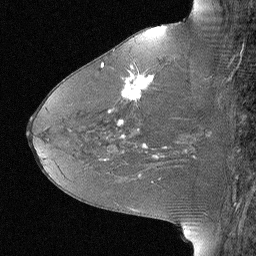
Breast MRI (dynamic contrast-enhanced), one sagittal slice. Position 31 of 64 along the scan axis. Dynamic contrast-enhanced study with each time point stored as its own series, time point 2 of 3 at this slice position (early post-contrast, ordered by acquisition time). 1.5 T. TE 4 ms, TR 30 ms. 256 × 256 image matrix. Female patient, age 46 years. From the clinical record (not read from this slice): setting: breast cancer imaged before/during neoadjuvant chemotherapy; receptor status: HR-positive, HER2-negative.
Structures marked on this image (semi-automatically segmented with operator editing):
- analysis volume of interest (the breast-tissue region the enhancement analysis was run in; not a lesion): bounding box <106,43,184,119> (left, top, right, bottom; pixels)
- tumour enhancement mask (voxels above the 90 % enhancement threshold inside the analysis volume of interest): <109,66,154,112>